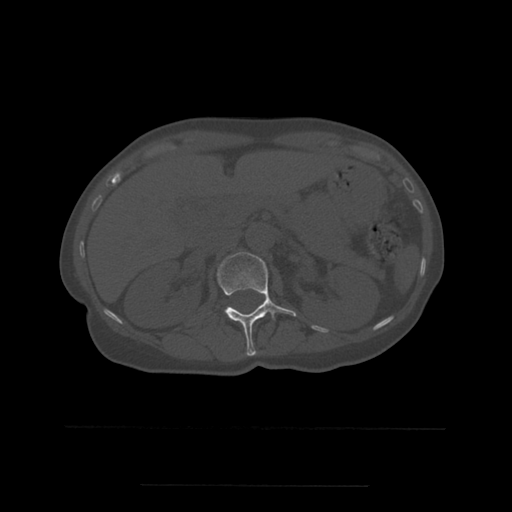
CT including the spine, one axial slice. Slice 233 of 544 in the series (ordered by position). Bone window (W 1800 / L 400 HU). 512 × 512 image matrix, field of view 350 × 350 mm. Patient age 58 years. Case-level facts recorded for this patient, not image findings: primary cancer: lung.
Structures marked on this image (semi-automatic segmentation, software-assisted and operator-edited):
- L1 vertebra: bounding box [x1, y1, x2, y2] px = [218, 253, 297, 356]